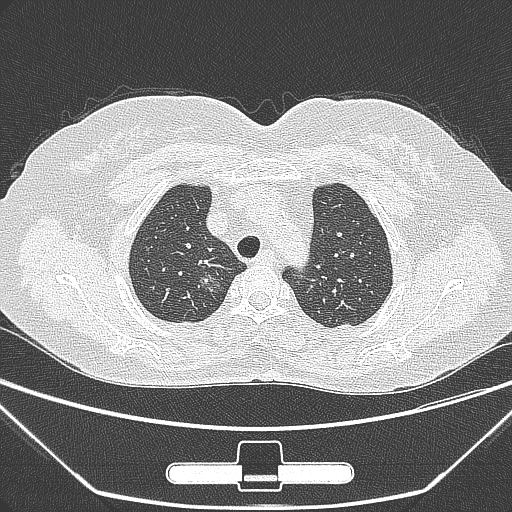
Chest CT, one axial slice. Position 227 of 275 along the scan axis. 120 kVp. Lung window (W 1500 / L -600 HU). 1 mm slice thickness. 512 × 512 image matrix. Patient: female, 63 years. Case-level facts recorded for this patient, not image findings: clinical TNM (as recorded): T1a N0 M0.
Outlined on this slice (rectangle marked by the reading radiologist):
- lung tumour (recorded histology: adenocarcinoma): bounding box [x1, y1, x2, y2] px = [197, 265, 228, 303]